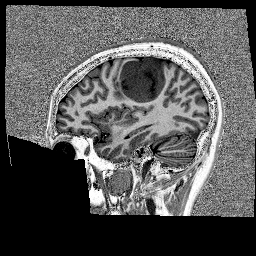
Brain MRI from a brain-tumour surgery series, one sagittal slice; position 53 of 176 along the scan axis; 256 × 256 image matrix, field of view 256 × 256 mm. From the clinical record (not read from this slice): histopathology: Glioblastoma; WHO grade: 4; IDH mutation: no; tumour location: Left Frontal.
Annotated regions visible in this slice (manually delineated by an expert):
- tumour: bounding box [x1, y1, x2, y2] px = [118, 58, 175, 105]